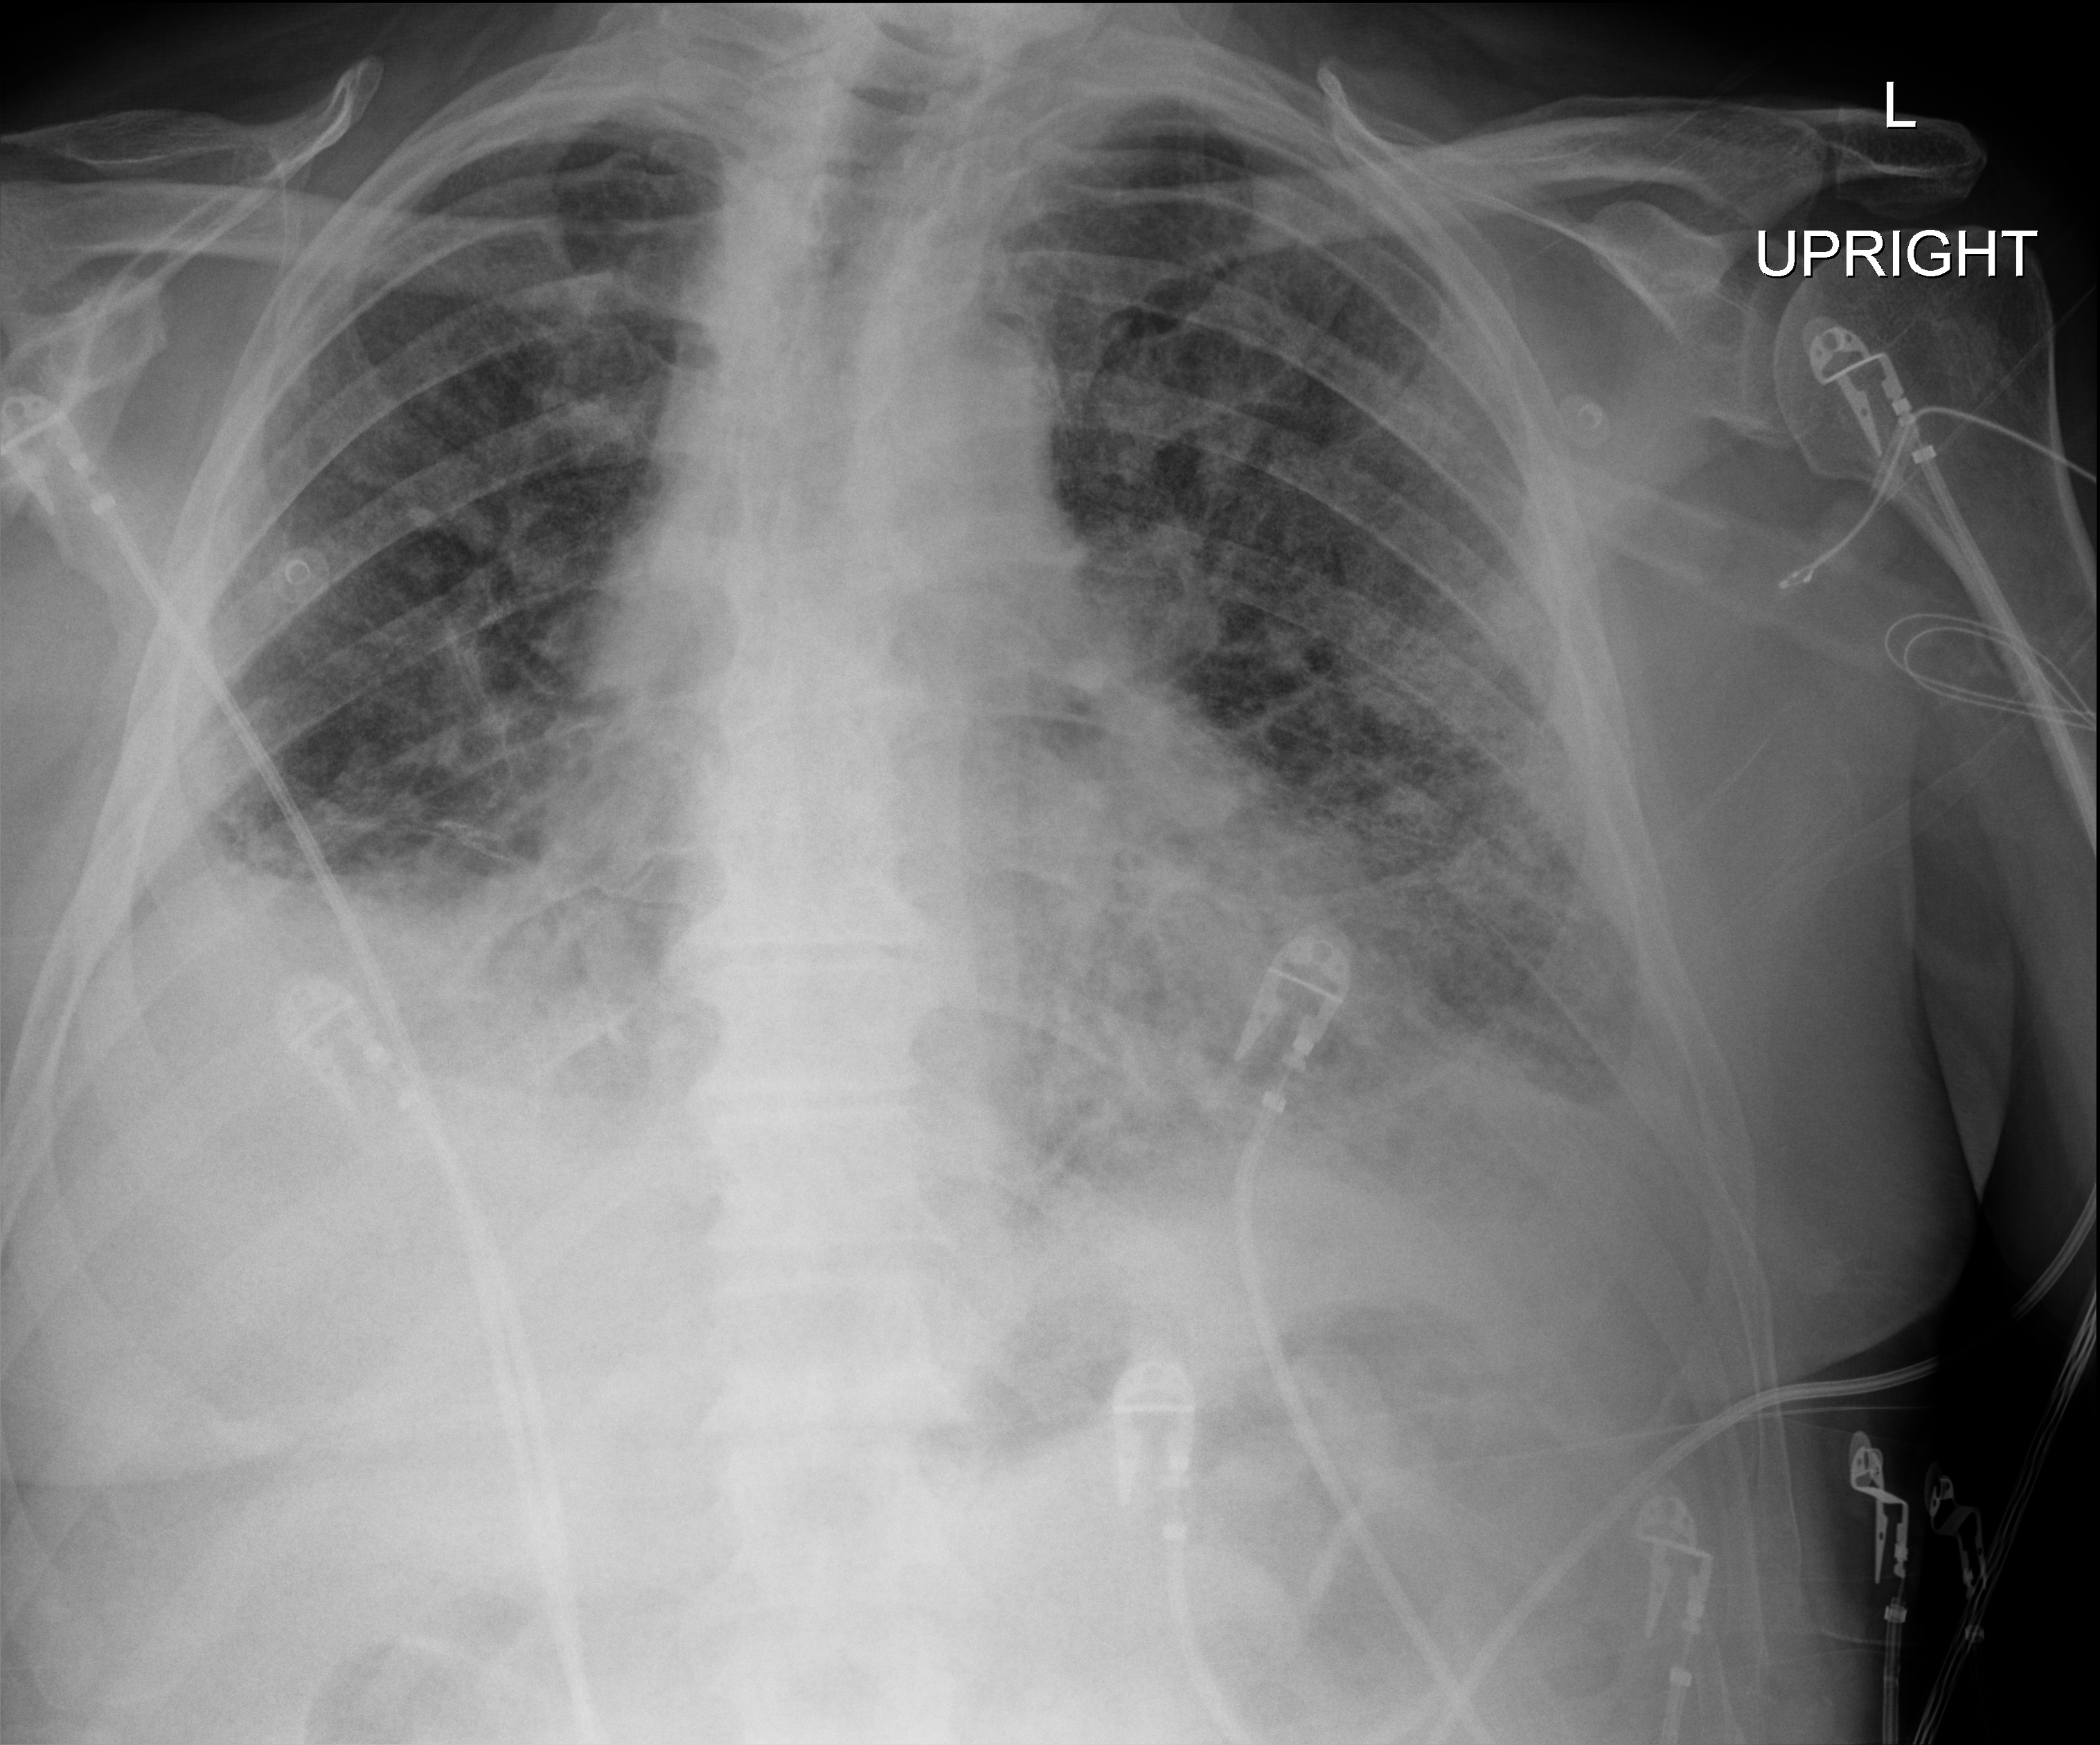
Bedside chest radiograph (digital radiography), anteroposterior (AP) projection. Patient hospitalised with COVID-19; male, aged 75–90 years.
Hospital-stay facts (about this admission, not read from this image; timing relative to this image not recorded): admitted to intensive care during this hospital stay: yes.